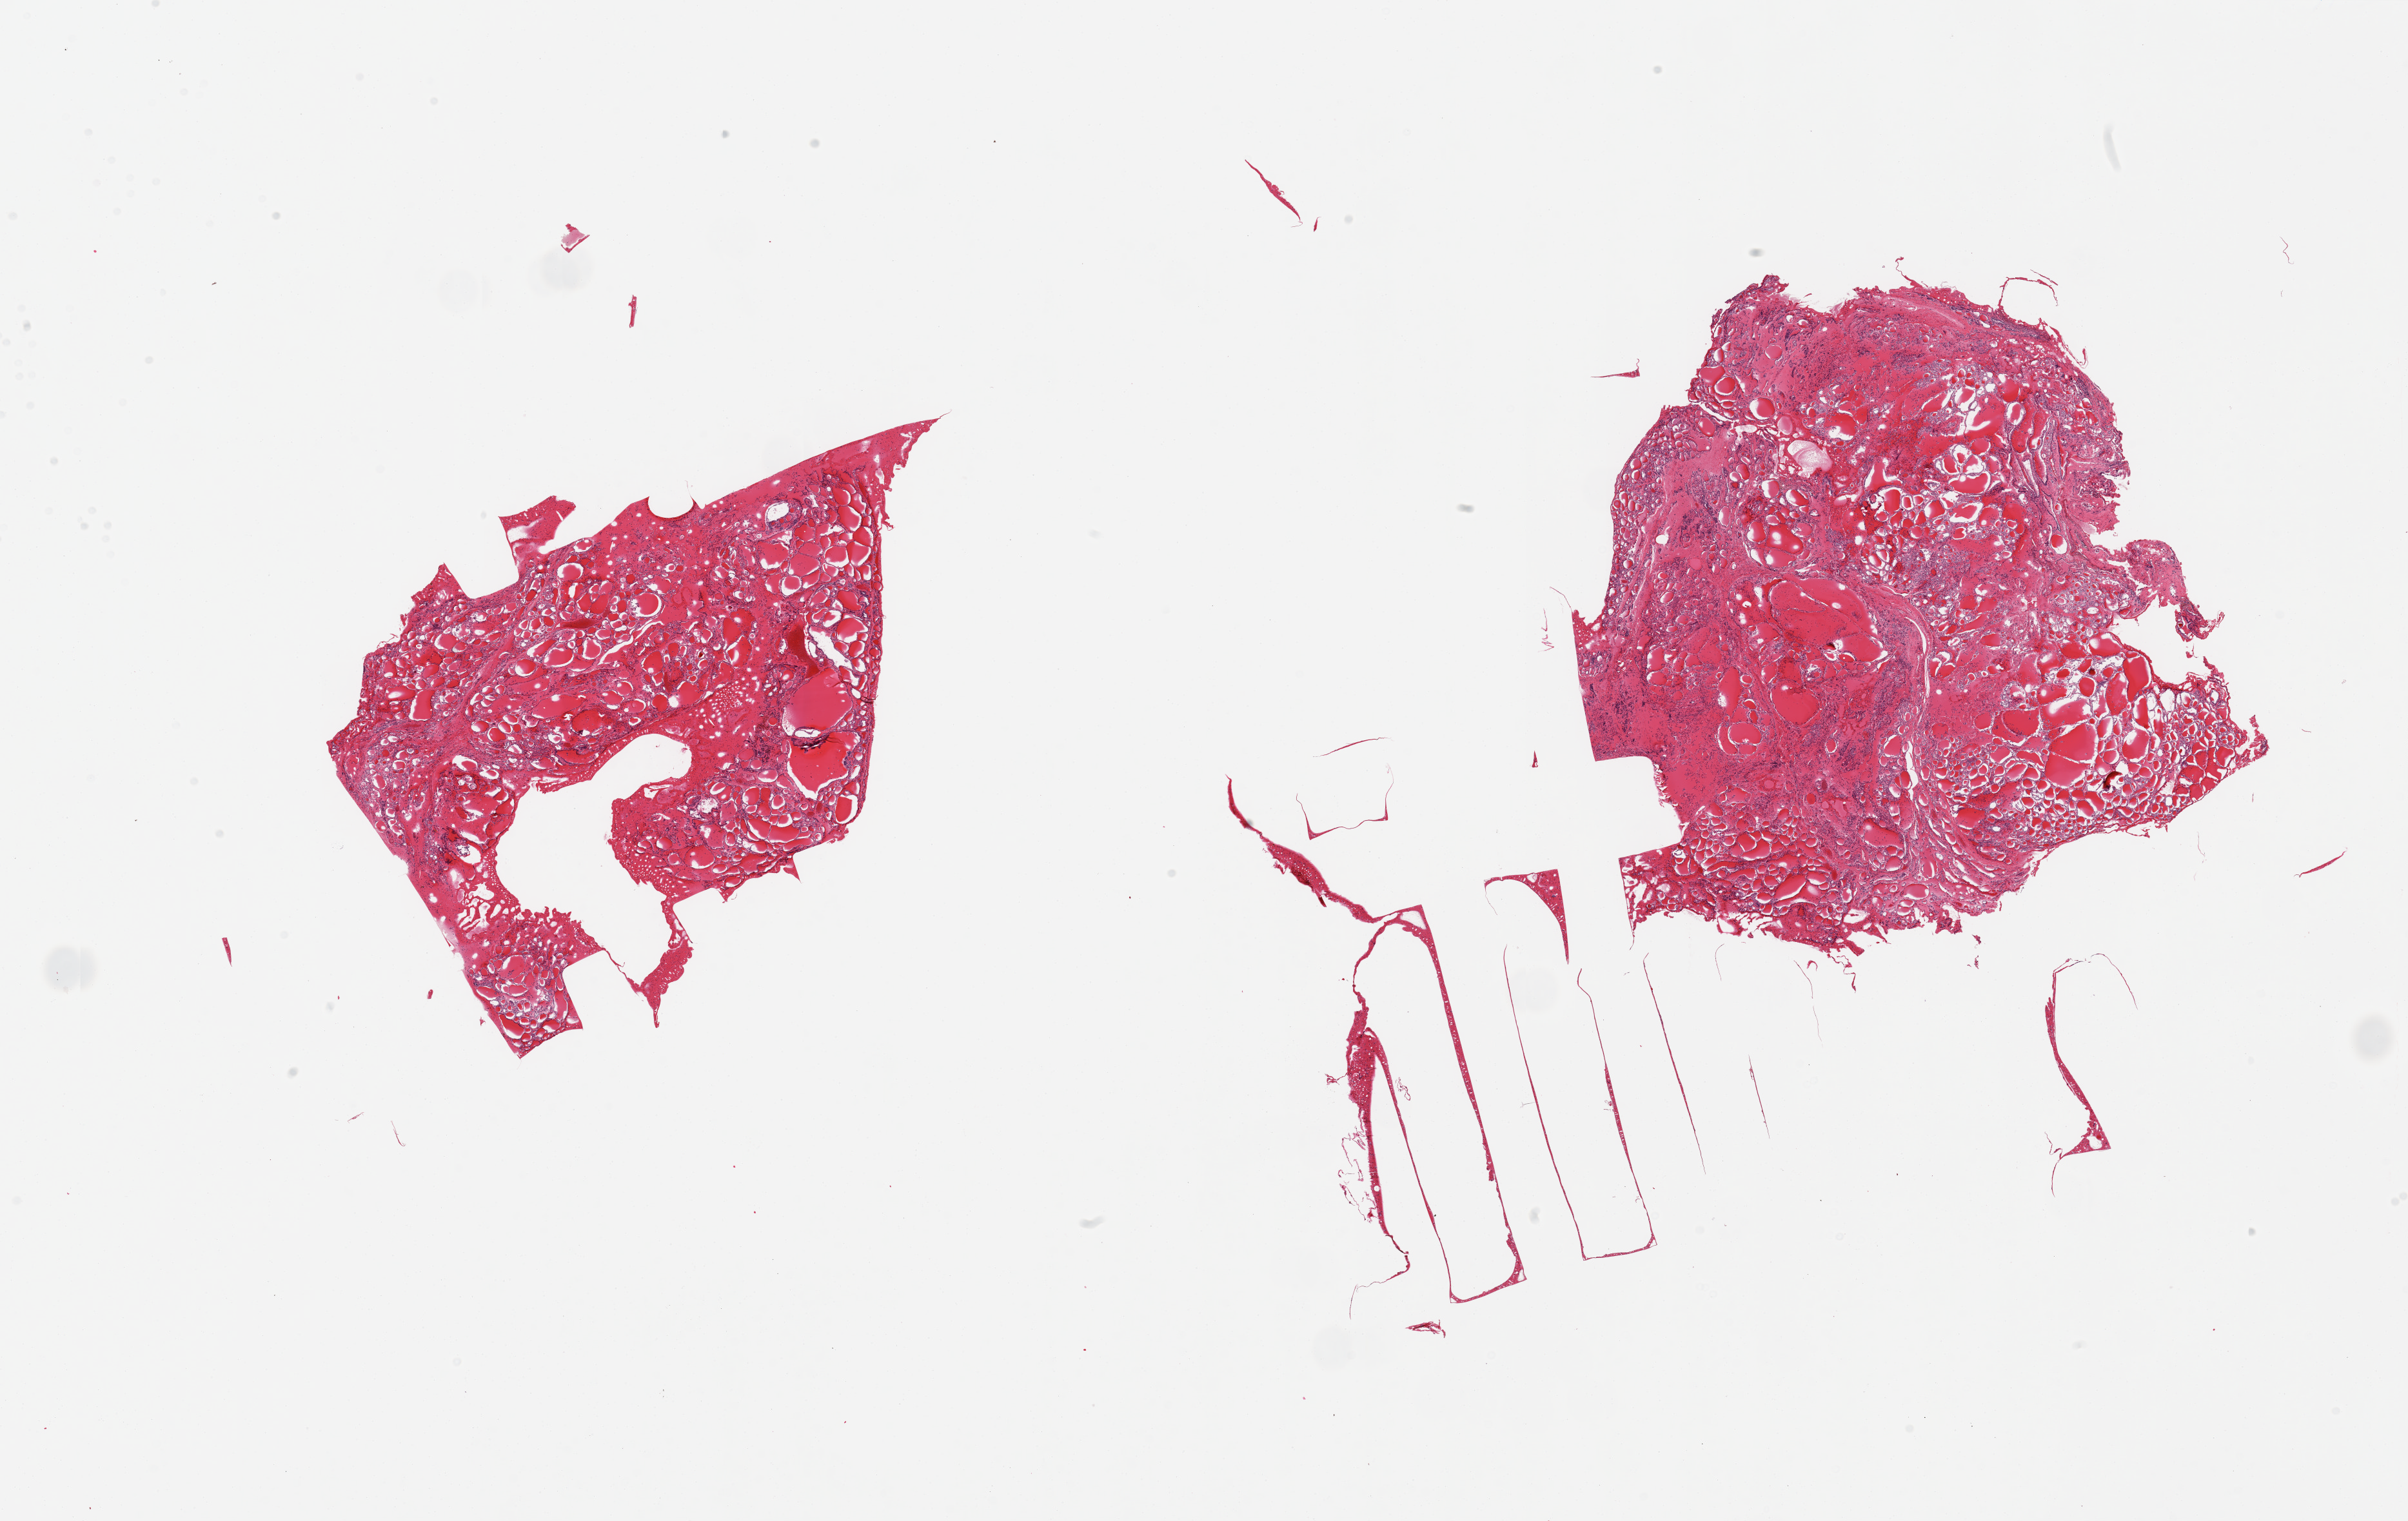
Whole-slide image, H&E stain — low-resolution overview of the scanned area, about 29.5 x 18.7 mm, PAXgene-fixed, paraffin-embedded tissue, section of thyroid (target tissue), donor tissue sample.
Review note (as recorded): 2 pieces; nodular hyperplasia.